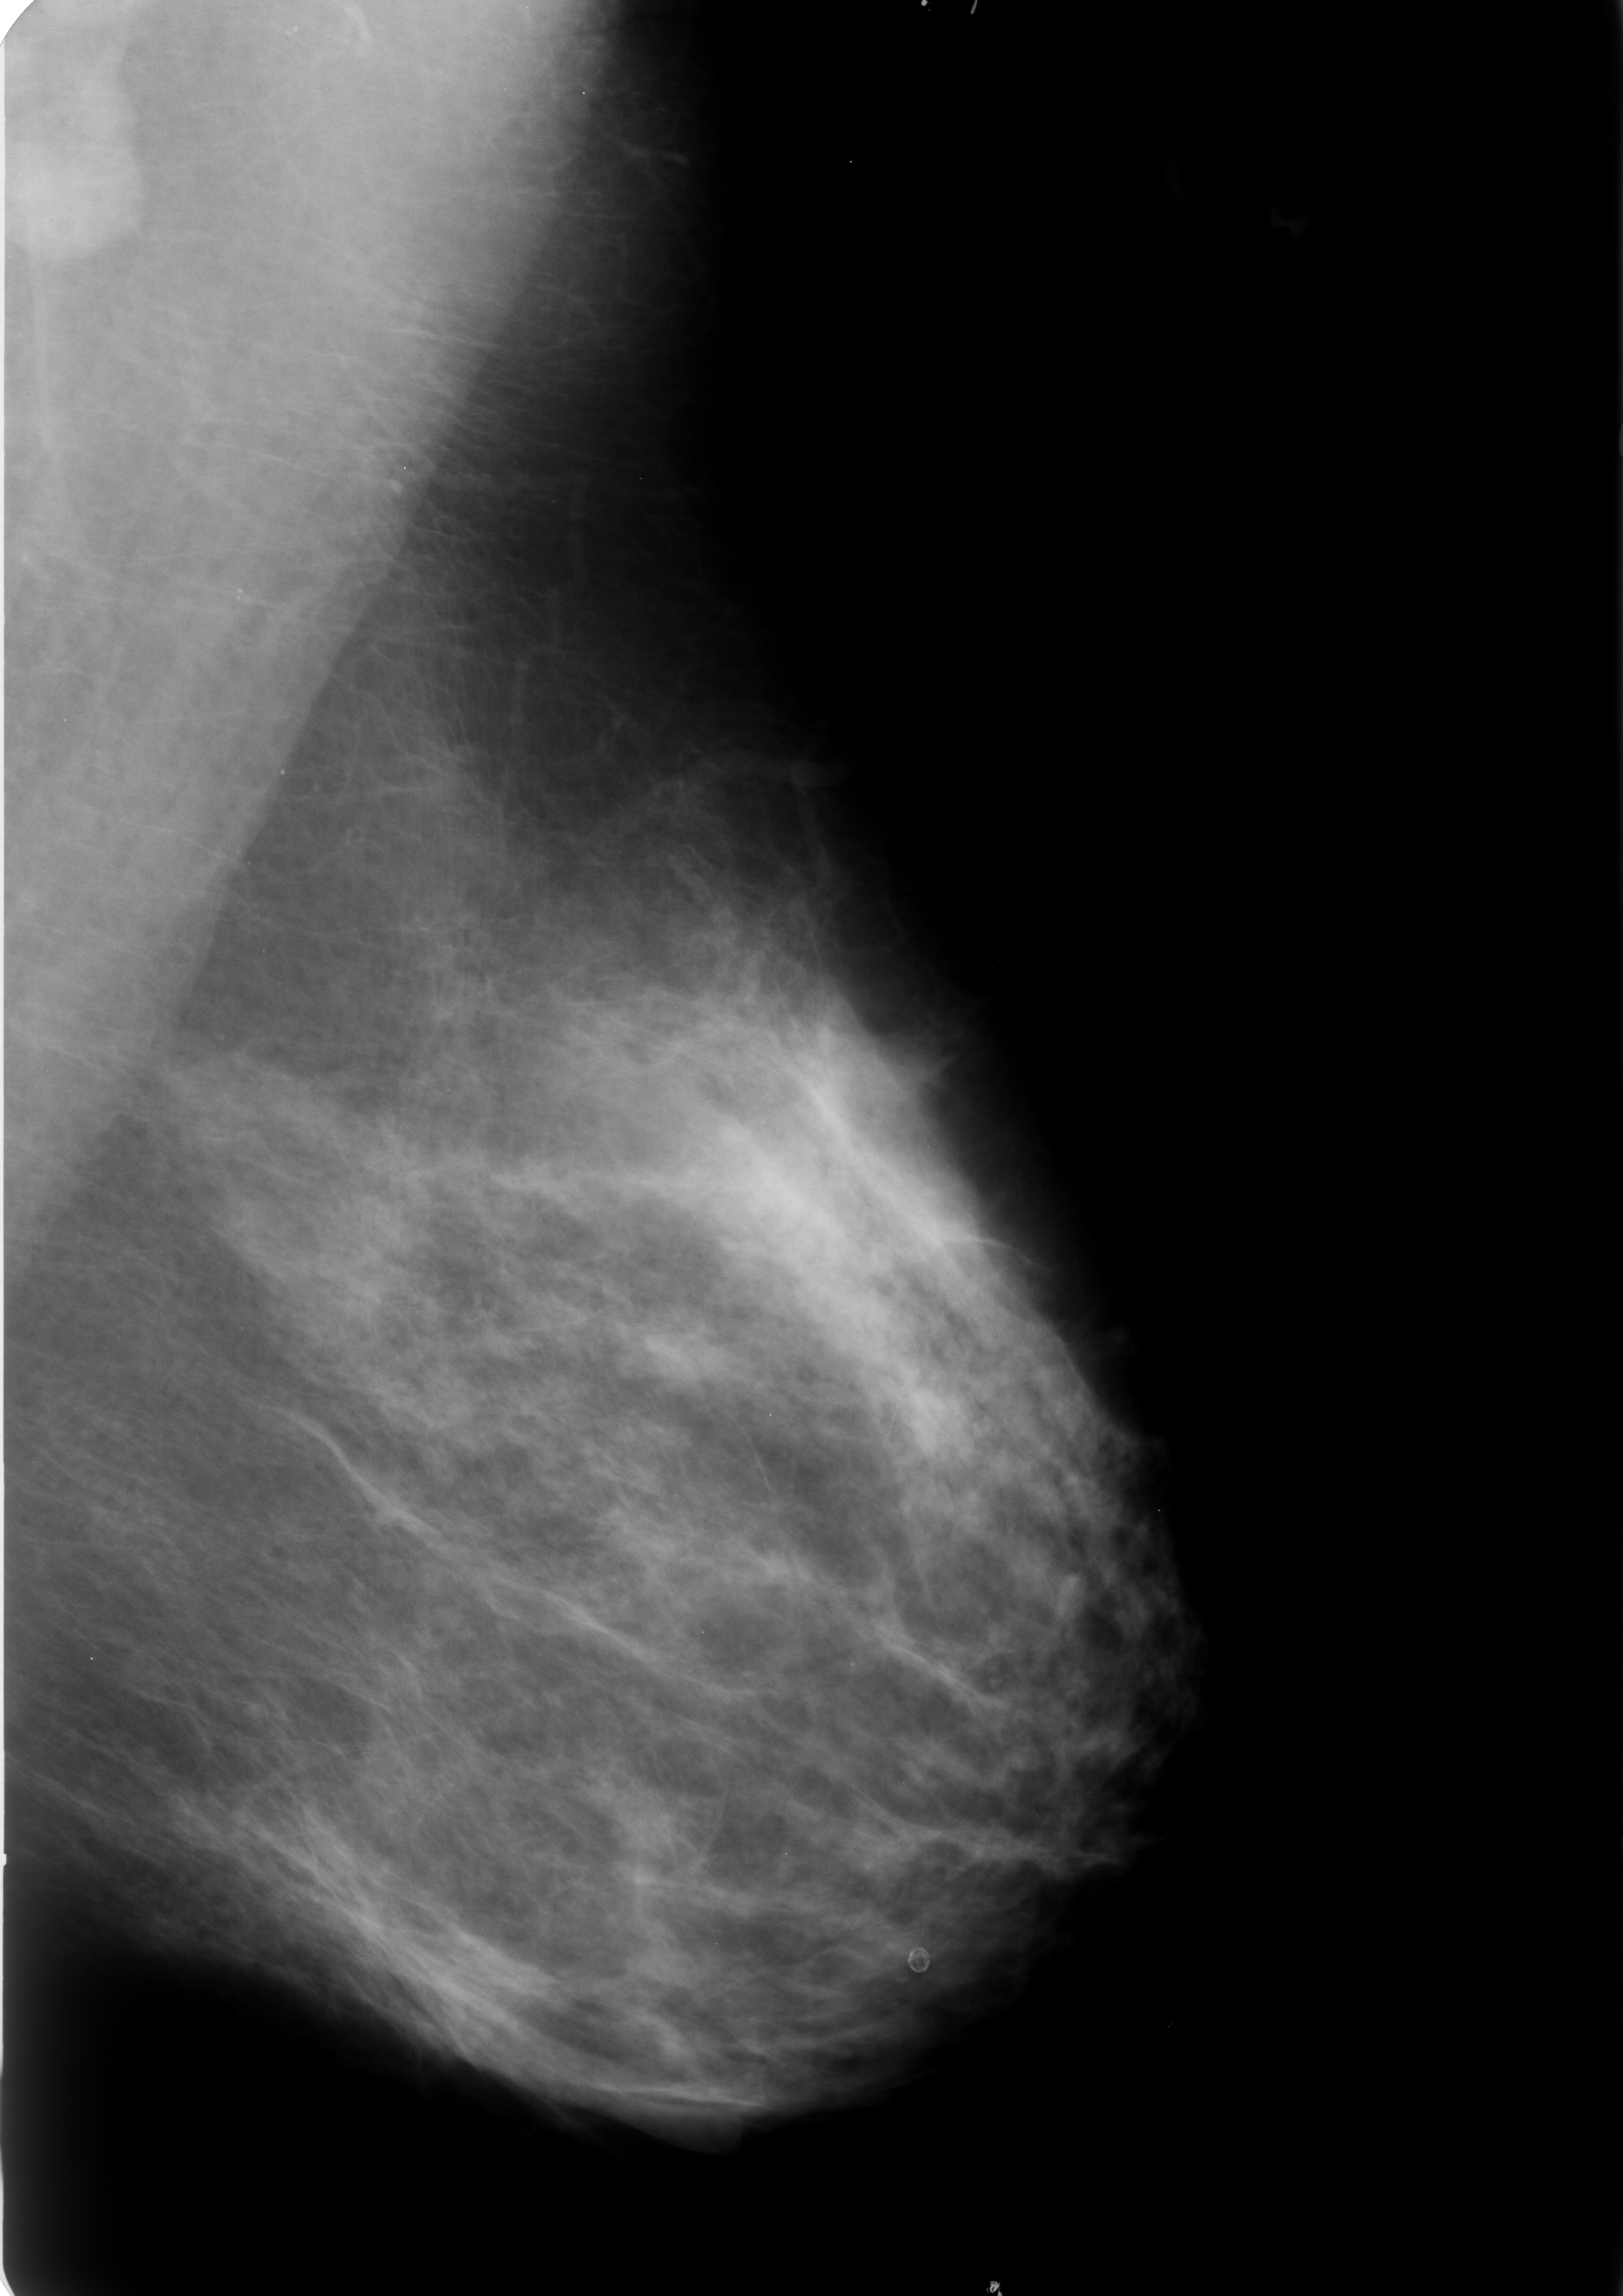
Scanned film-screen mammogram; left breast; mediolateral oblique (MLO) view; breast composition: scattered fibroglandular densities (BI-RADS density category 2 of 4).
Marked abnormality: calcifications, morphology lucent center; BI-RADS assessment category 2; subtlety rating 5 on a 1 (subtle) to 5 (obvious) scale; benign without callback (not worked up further).